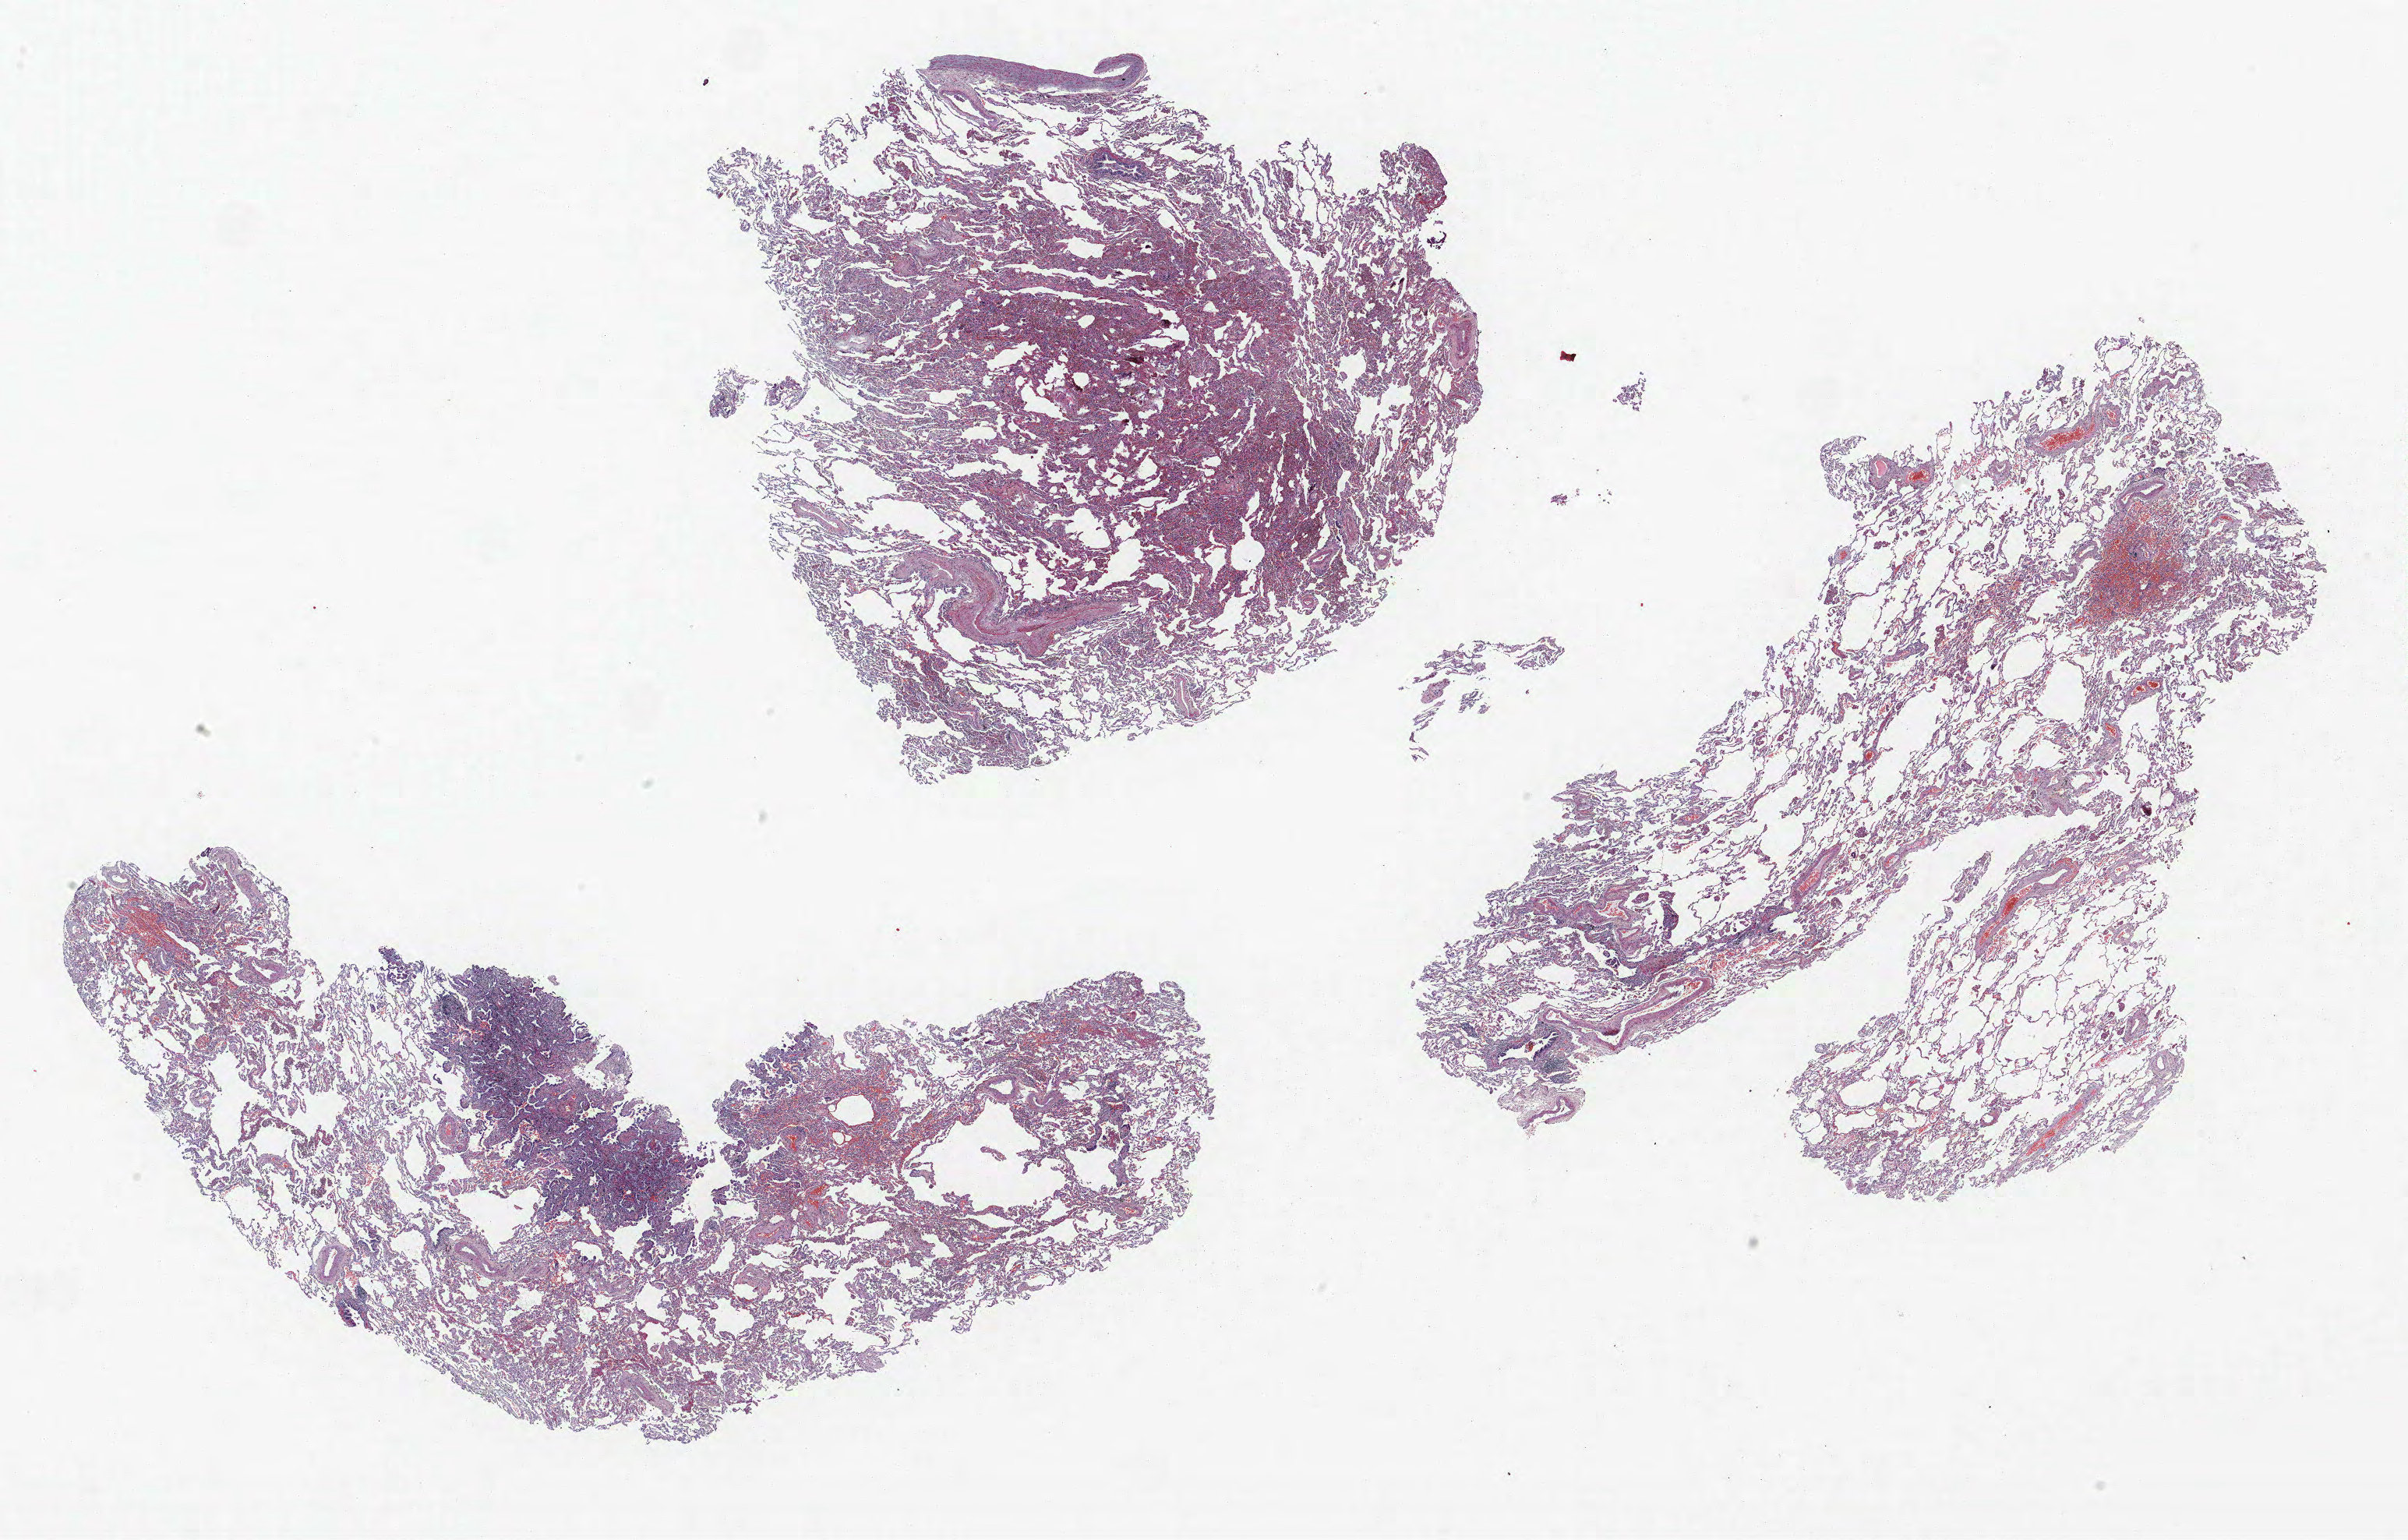
H&E-stained whole-slide image, low-resolution overview of the scanned area, about 24.7 x 15.8 mm (slide scanned at 40x), FFPE section, lung. Female patient, aged 63 at enrolment. Current smoker at enrolment. Grade: well differentiated (G1).
Tumour size (pathology): 90 mm. Participant's lung-cancer diagnosis: Adenocarcinoma, NOS. Primary tumour location (clinical record): right upper lobe. Stage (AJCC 6th edition): IA.